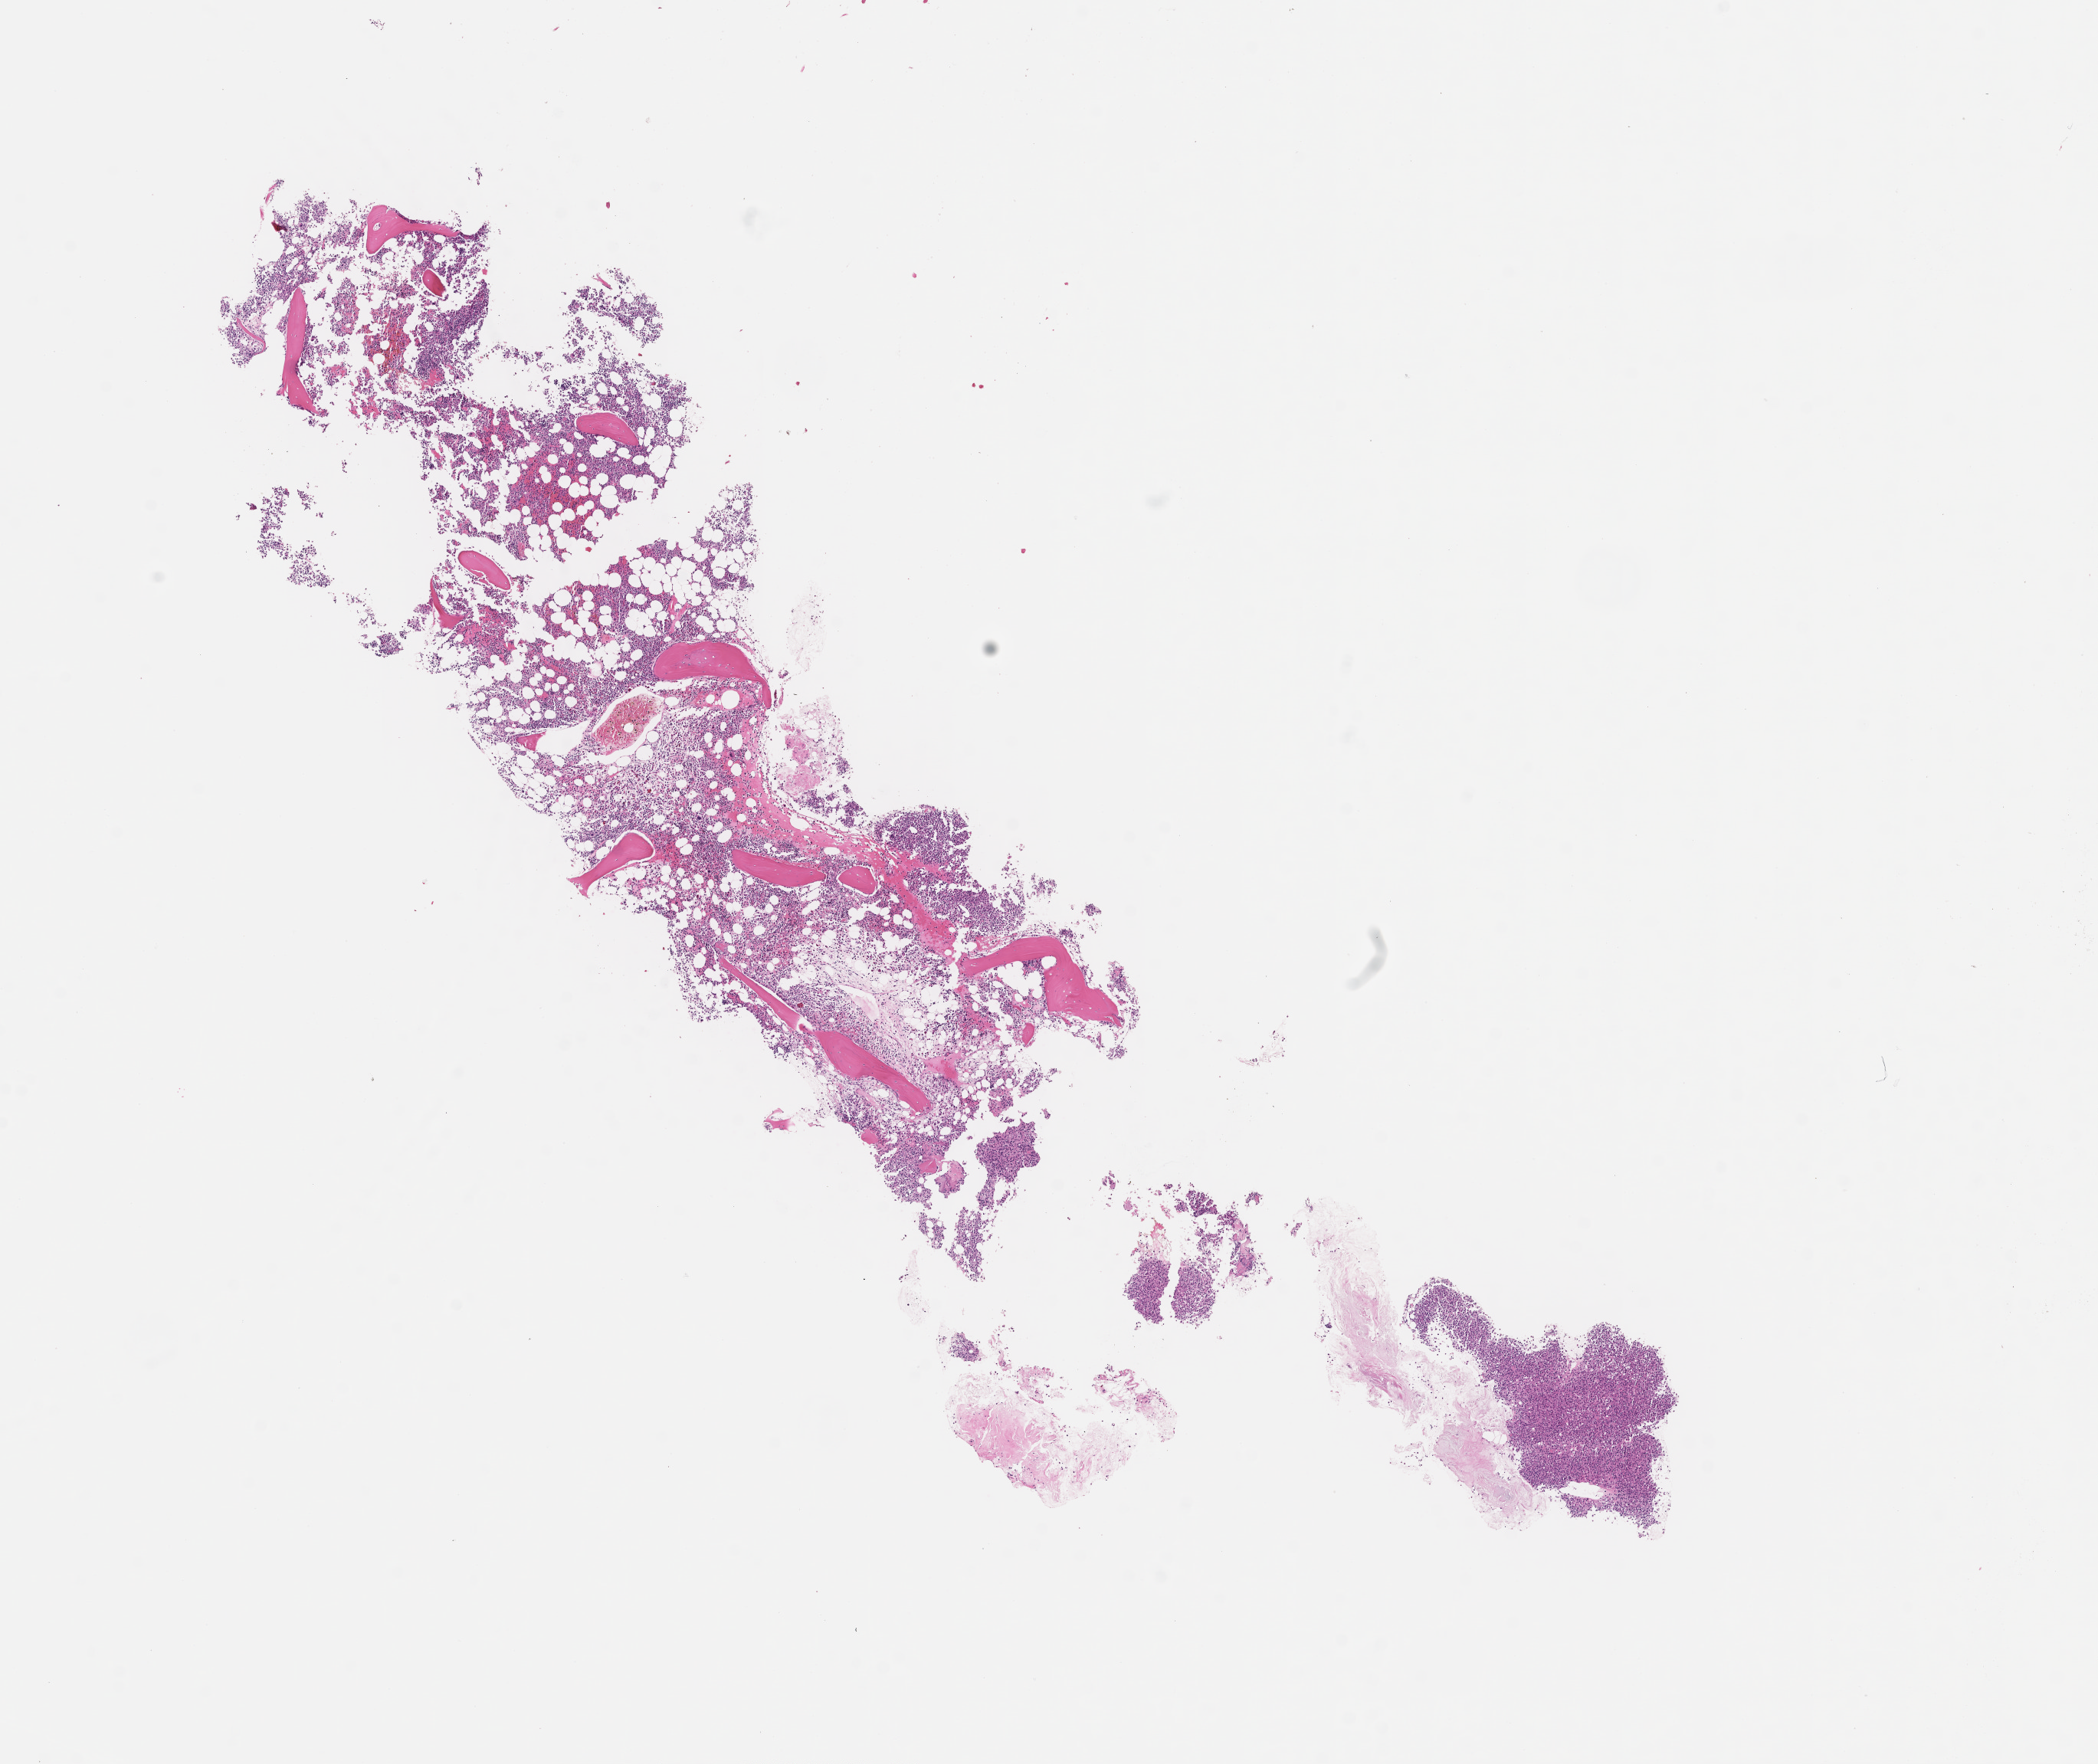
Hematoxylin and eosin (H&E) whole-slide image — shown as a low-resolution overview of the whole scanned area (about 11.1 x 9.3 mm); formalin-fixed, paraffin-embedded (FFPE) tissue; tissue site: bone marrow. Female patient.
This section: primary tumour tissue. Diagnosis: Plasma Cell Myeloma.